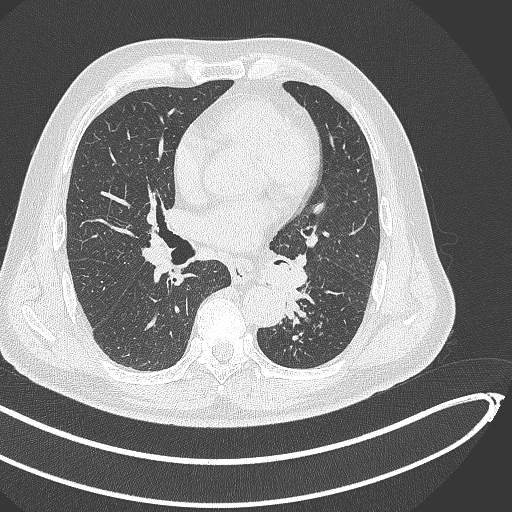
Chest CT, one axial slice; reconstruction kernel B70f; 120 kVp; lung window (W 1500 / L -600 HU); 1 mm slice thickness; 512 × 512 image matrix, field of view 400 × 400 mm. Patient: male, 64 years. Case-level facts recorded for this patient, not image findings: clinical TNM (as recorded): T1c N0 M0; histopathological grade: G2.
Annotated regions visible in this slice (rectangle marked by the reading radiologist):
- lung tumour (recorded histology: squamous cell carcinoma): bounding box <262,253,308,318> (left, top, right, bottom; pixels)